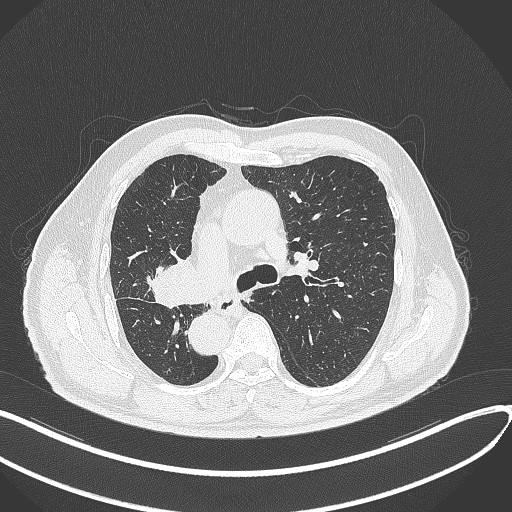
Chest CT, one axial slice. Position 193 of 300 along the scan axis. Lung window (W 1500 / L -600 HU). 1 mm slice thickness. 512 × 512 image matrix, field of view 400 × 400 mm. Patient: male, 67 years. Case-level facts recorded for this patient, not image findings: clinical TNM (as recorded): T2a N0 M0.
Structures marked on this image (bounding box drawn by a radiologist):
- lung tumour (recorded histology: squamous cell carcinoma): bounding box (x1, y1, x2, y2) in pixels: (142, 248, 211, 309)